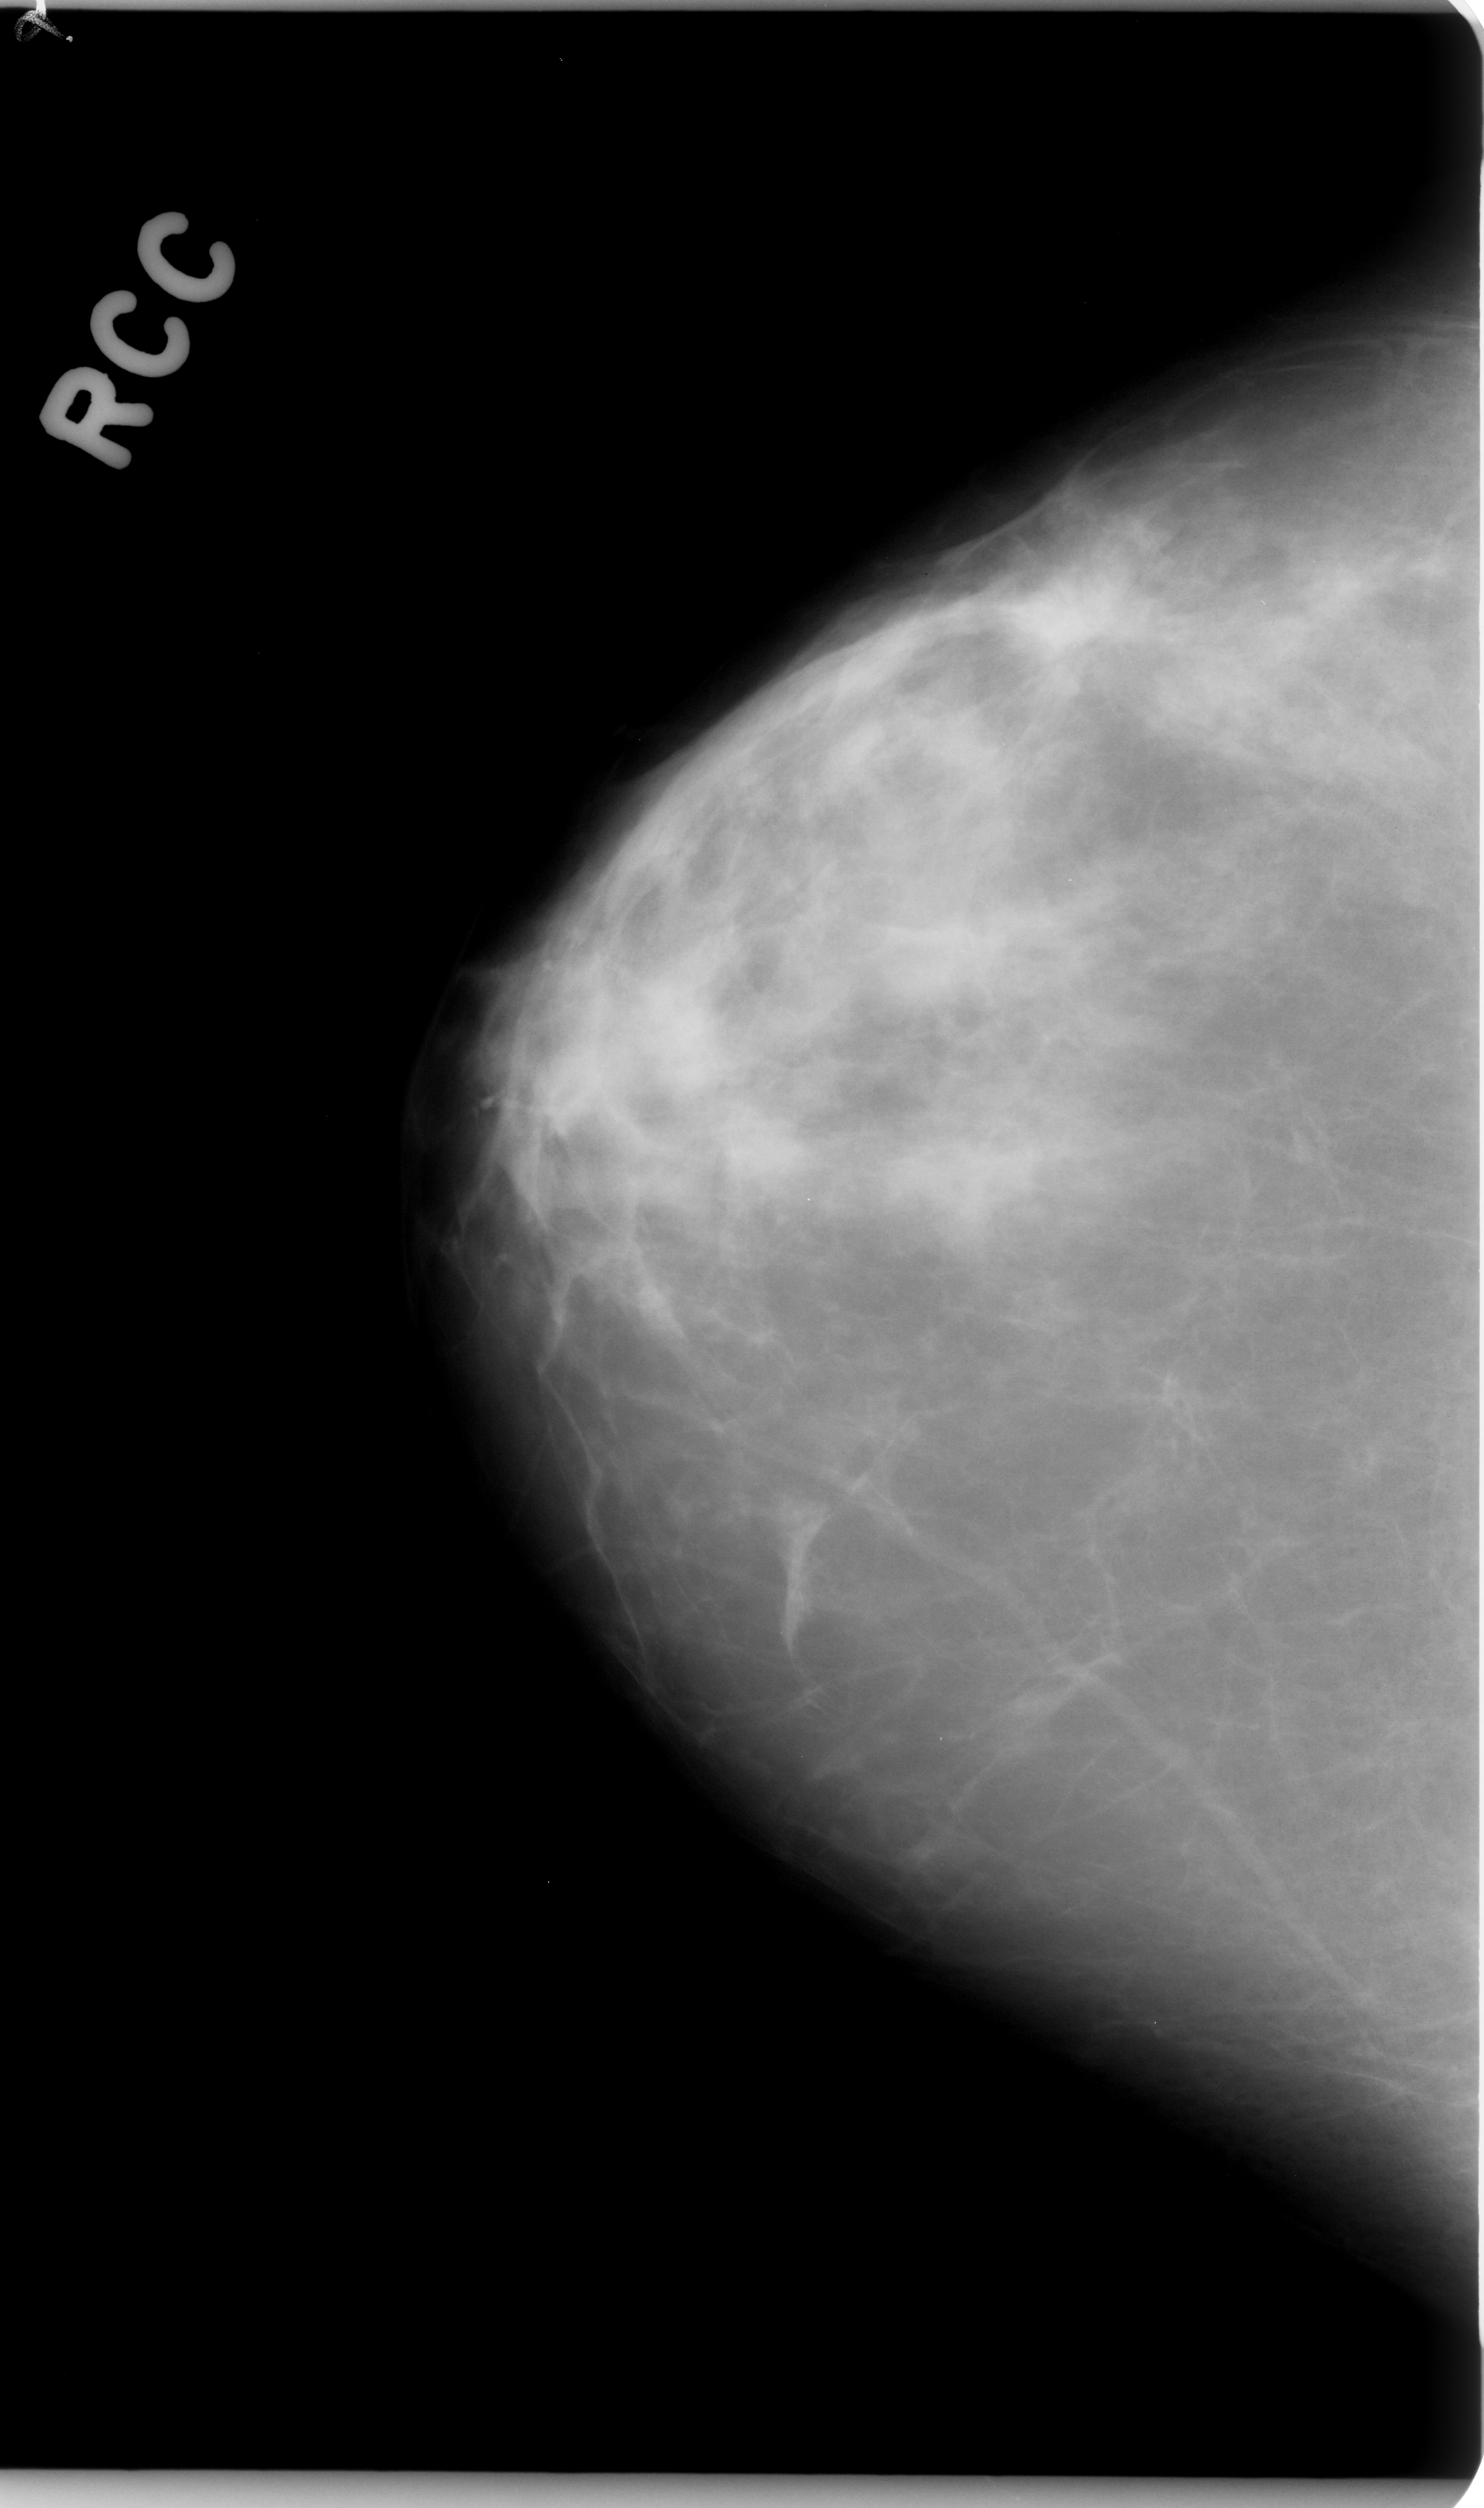
Mammogram (digitized film); right breast; CC view; breast composition: scattered fibroglandular densities (BI-RADS density category 2 of 4); 1484 × 2508 image matrix.
Expert-marked regions of interest on this image (one box per marked abnormality):
- mass, shape irregular, margins spiculated; BI-RADS assessment category 5; subtlety rating 5 on a 1 (subtle) to 5 (obvious) scale; pathology (as recorded): malignant: bounding box (x1, y1, x2, y2) in pixels: (976, 527, 1183, 725)